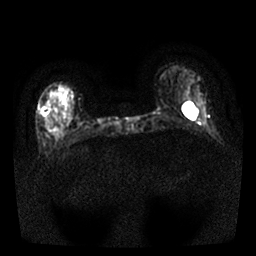
Breast MRI, one axial slice. Slice 7 of 25 in the series (ordered by position). Diffusion-weighted series; image 2 of 4 stored at this slice position (different b-values; order by instance number). 1.5 T. 4 mm slice thickness. 256 × 256 image matrix. Female patient.
Structures marked on this image (expert manual segmentation):
- tumour on diffusion-weighted imaging: box from (x=41, y=107) to (x=49, y=116) px